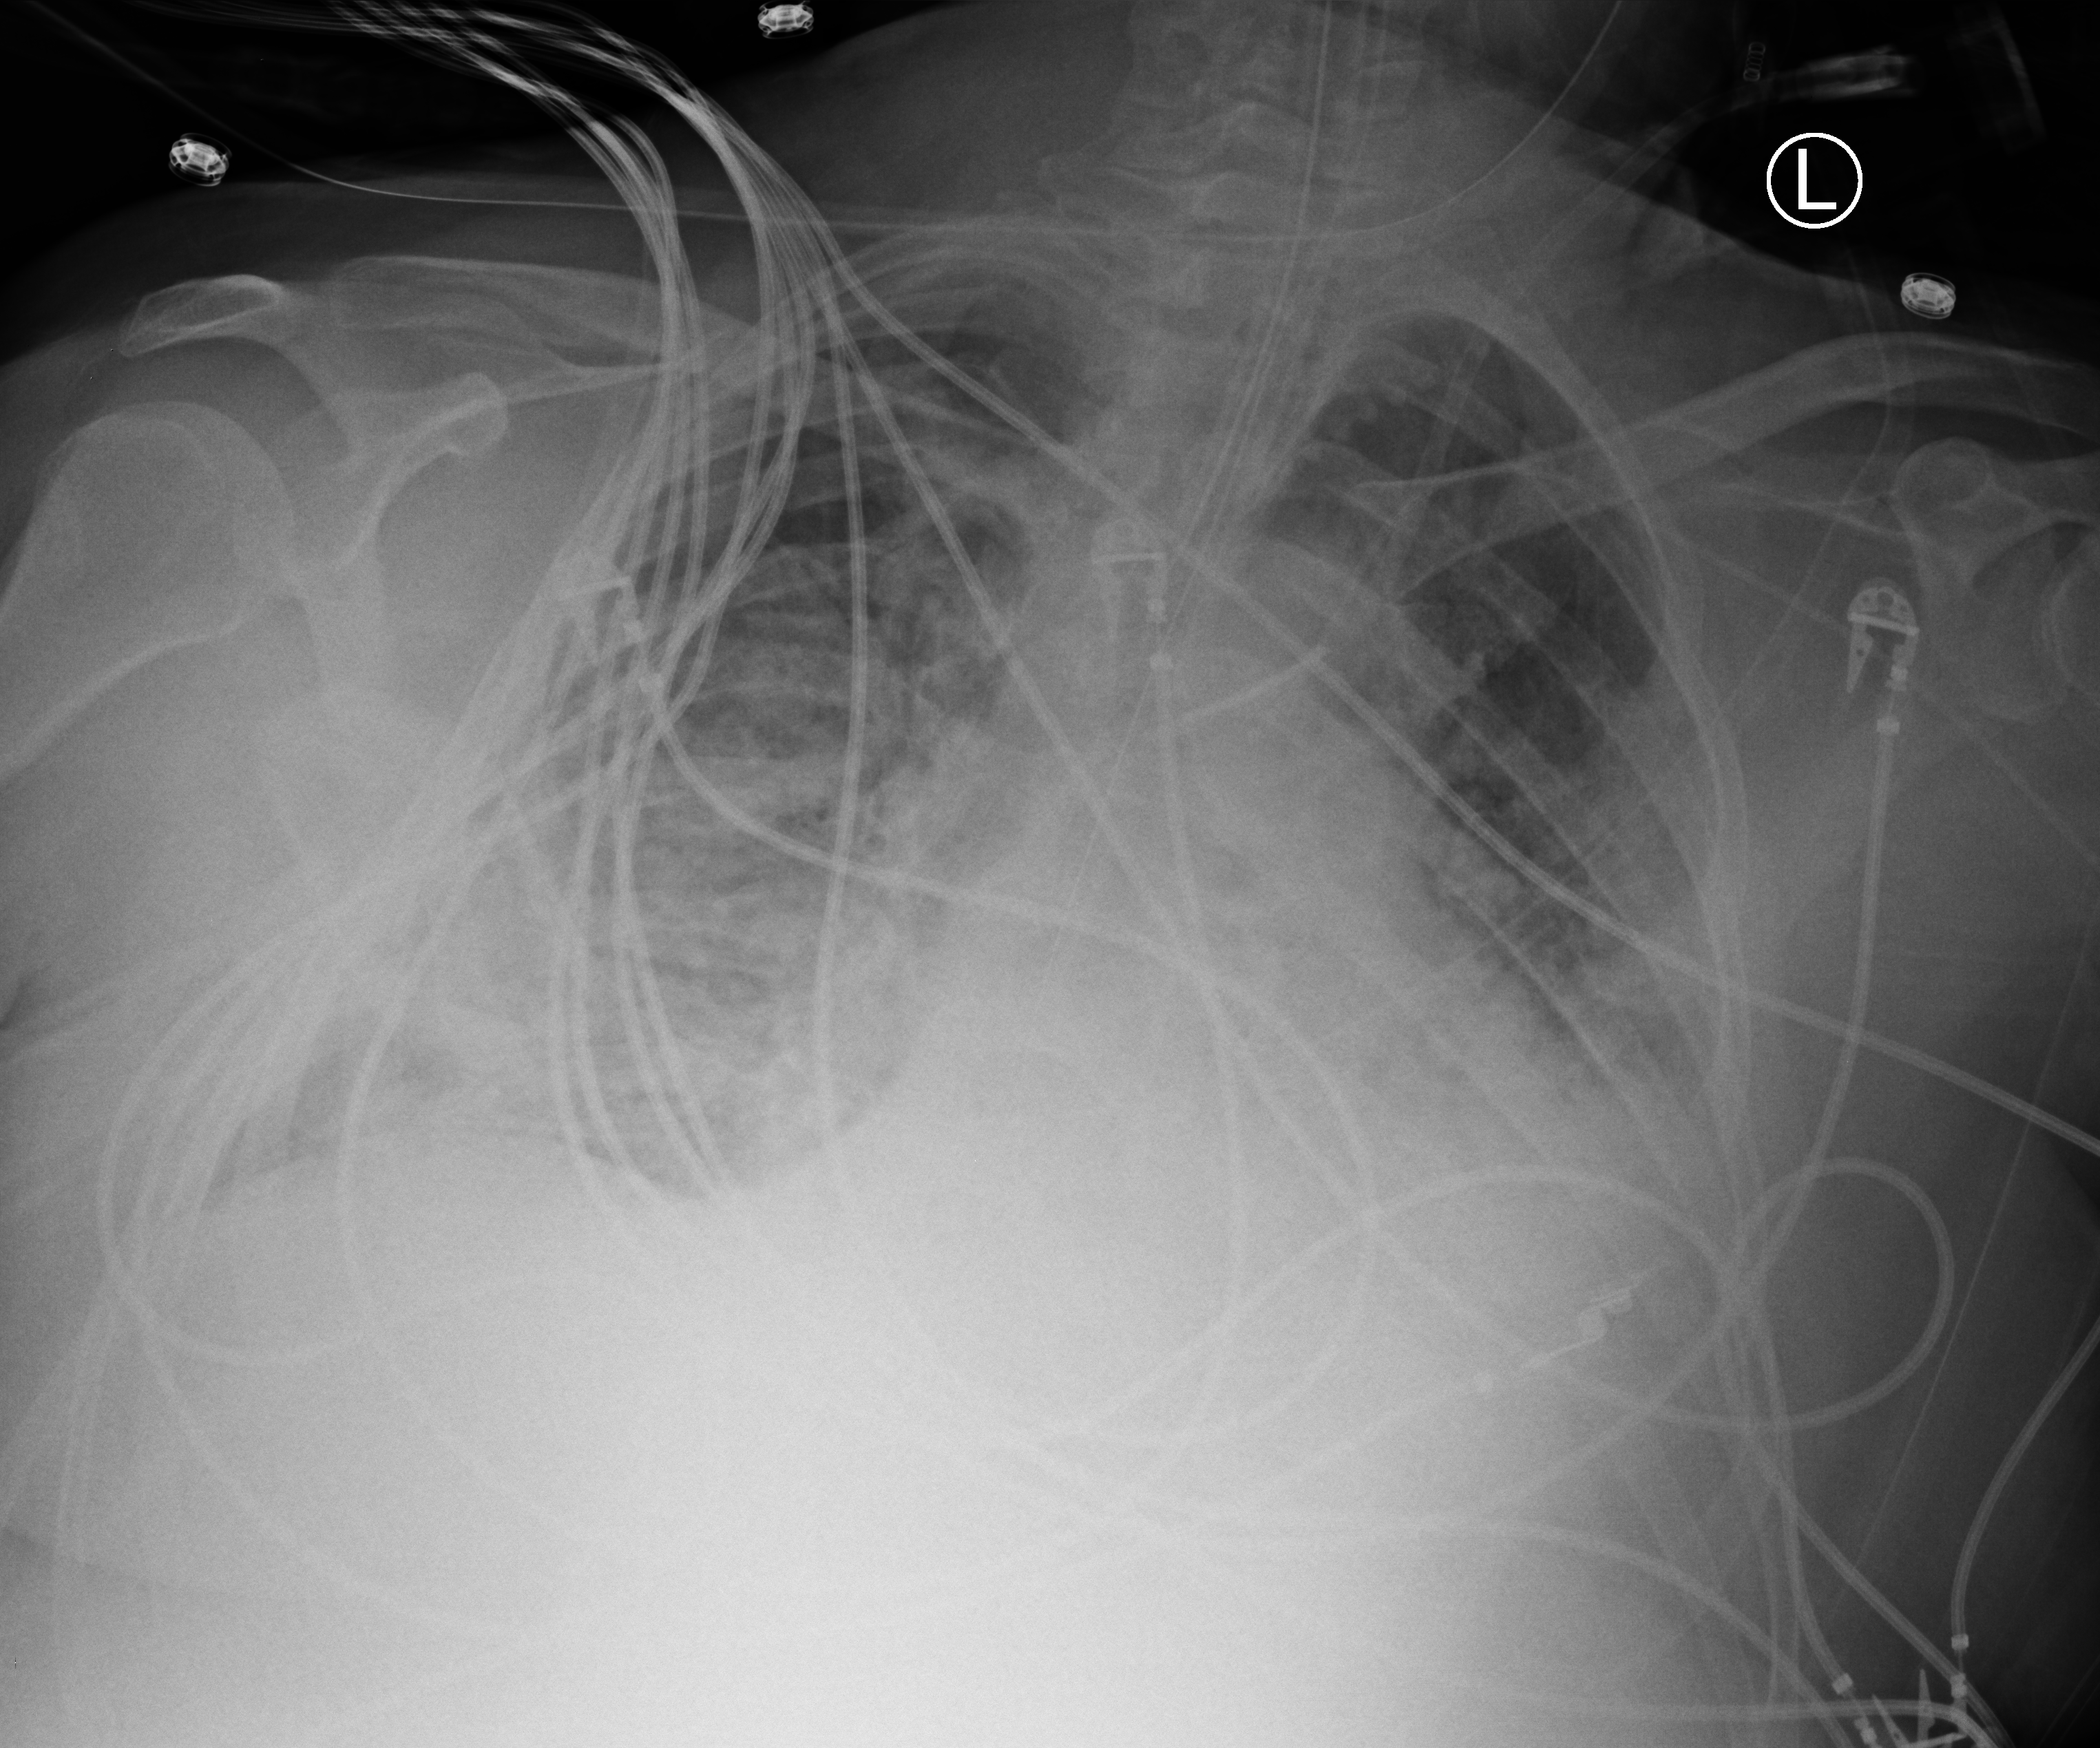
Portable chest radiograph, anteroposterior (AP) projection. Patient hospitalised with COVID-19; male, aged 18–59 years.
Admission-level facts for this patient (not findings on this image; timing relative to this image not recorded): mechanically ventilated during this hospital stay: yes; chronic kidney disease (admission record): no; COPD (admission record): no.